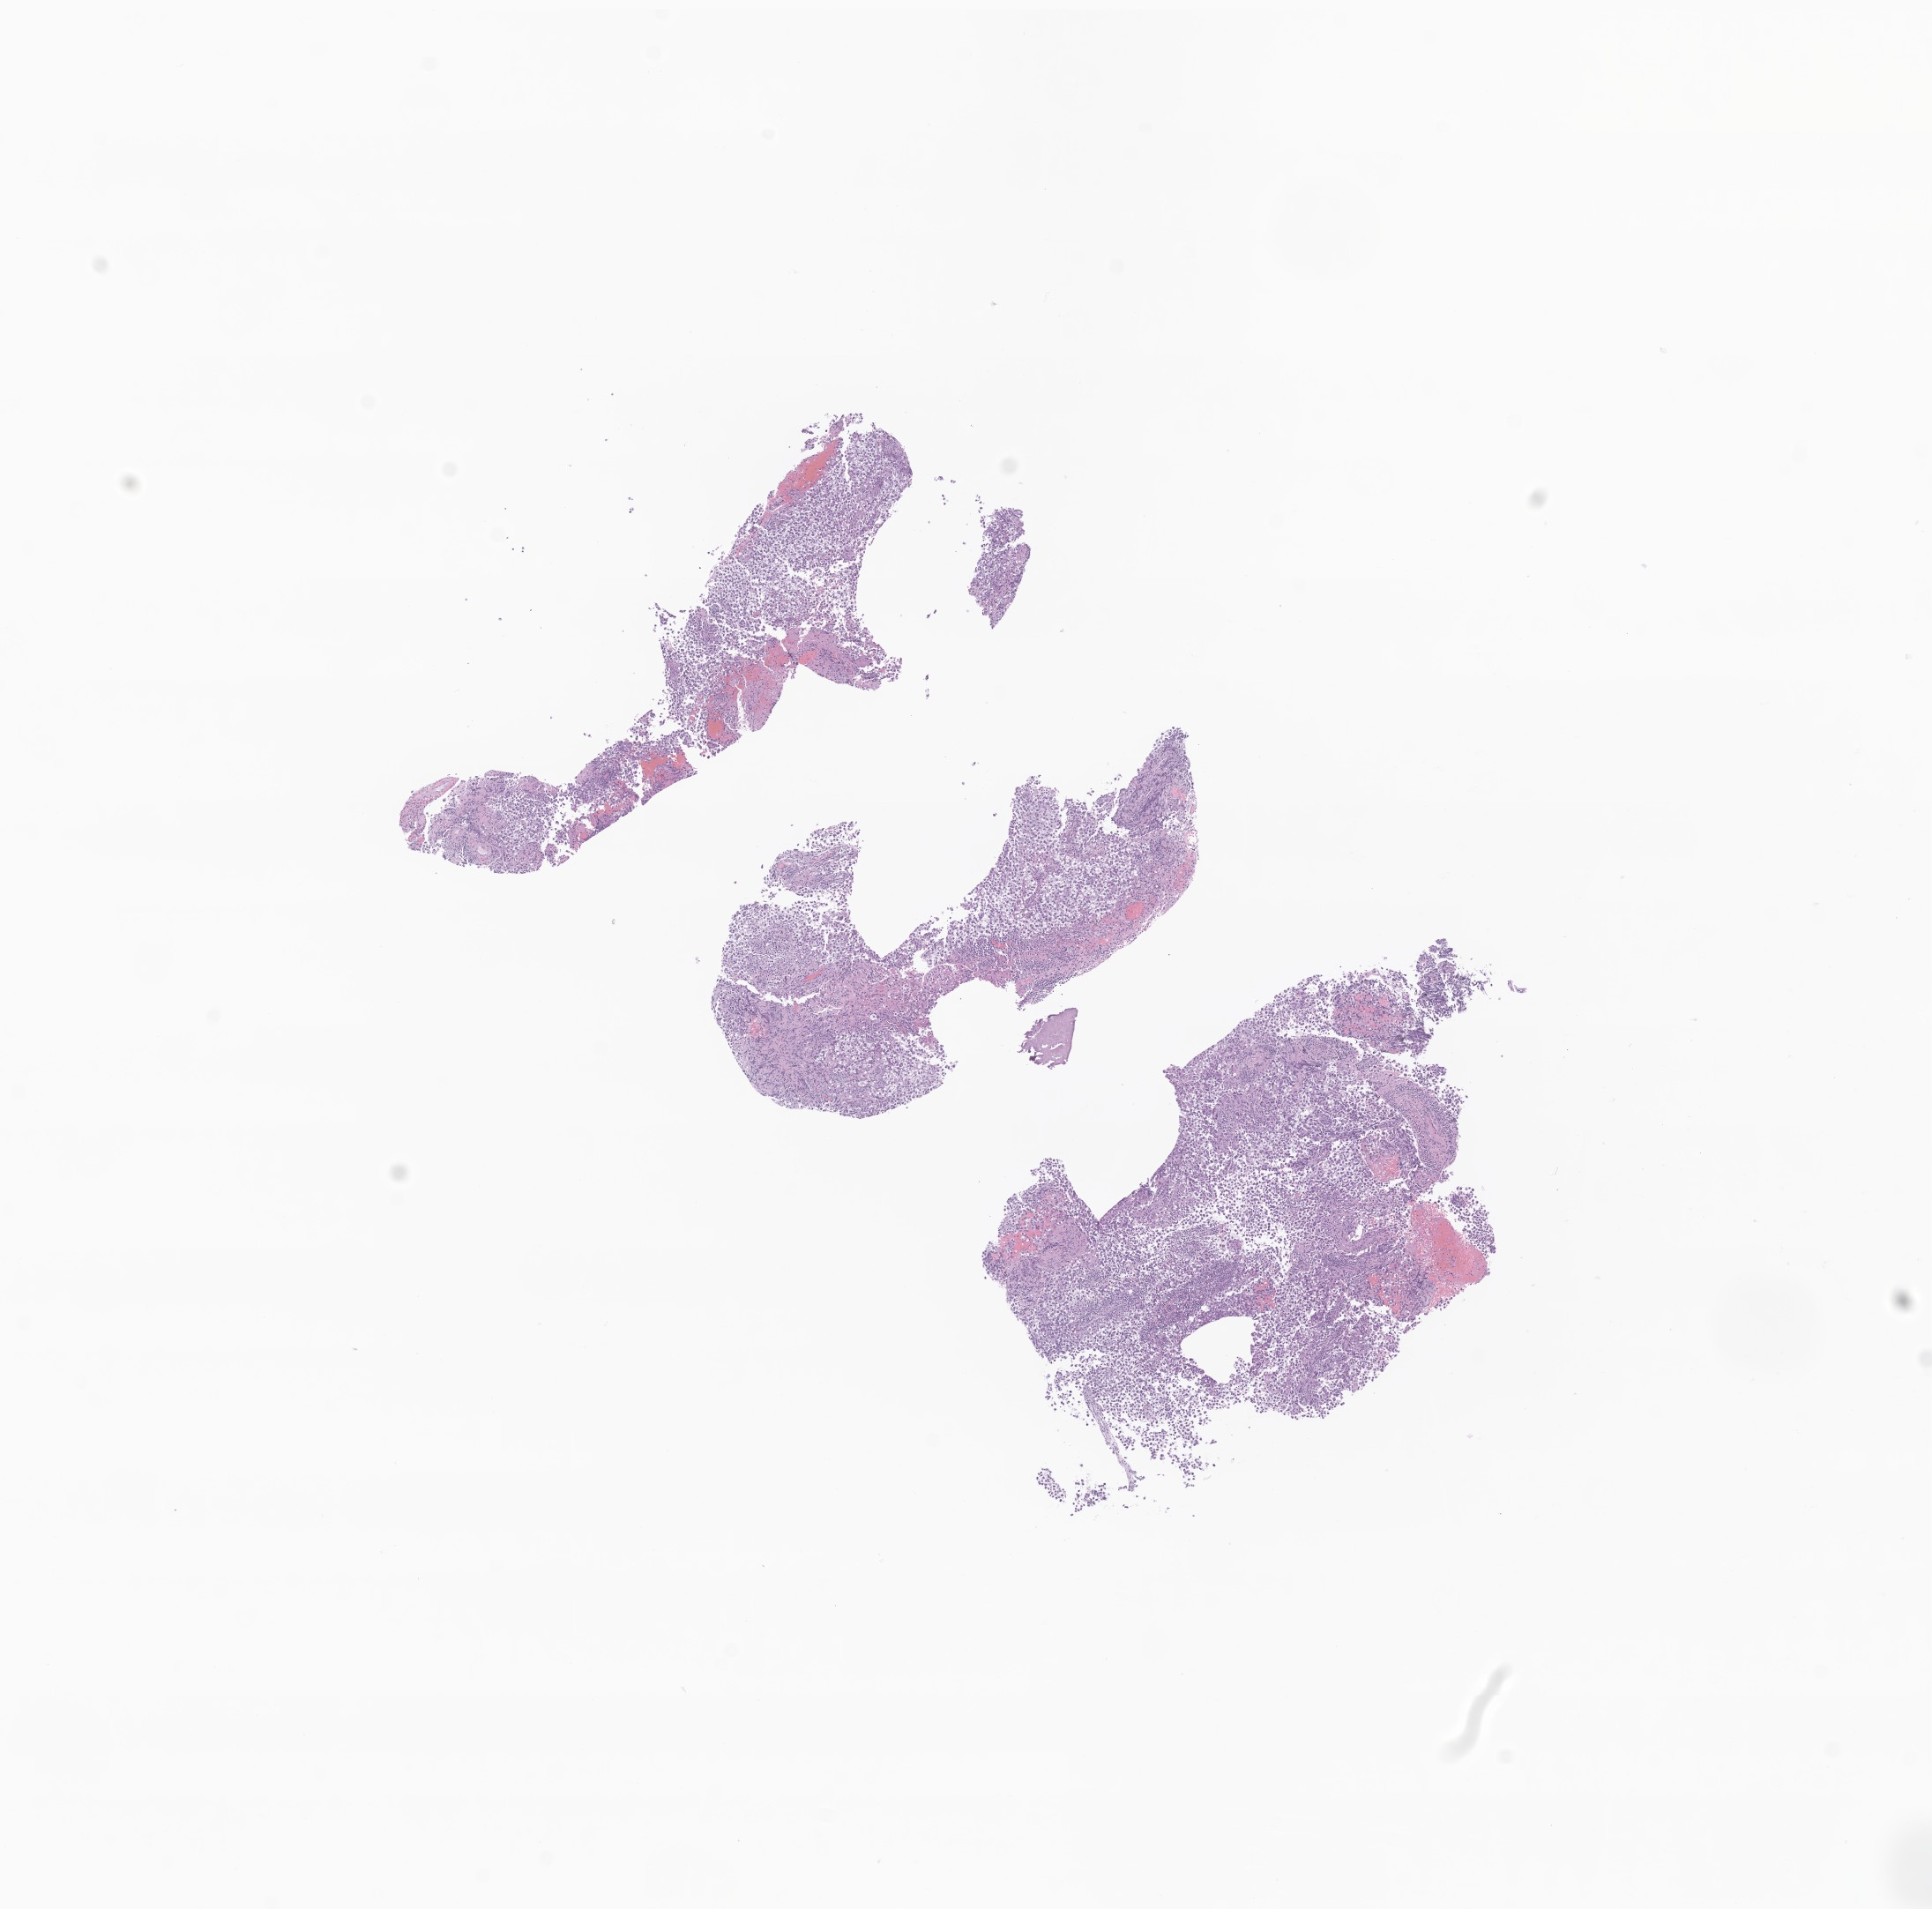
Whole-slide image, hematoxylin and eosin (H&E) stain of tumor tissue from the brain — a low-resolution overview of the entire scanned area, about 9.2 x 9.1 mm. FFPE section. Male patient, age 153 months (12 years 9 months).
Recorded diagnosis: Germinoma.